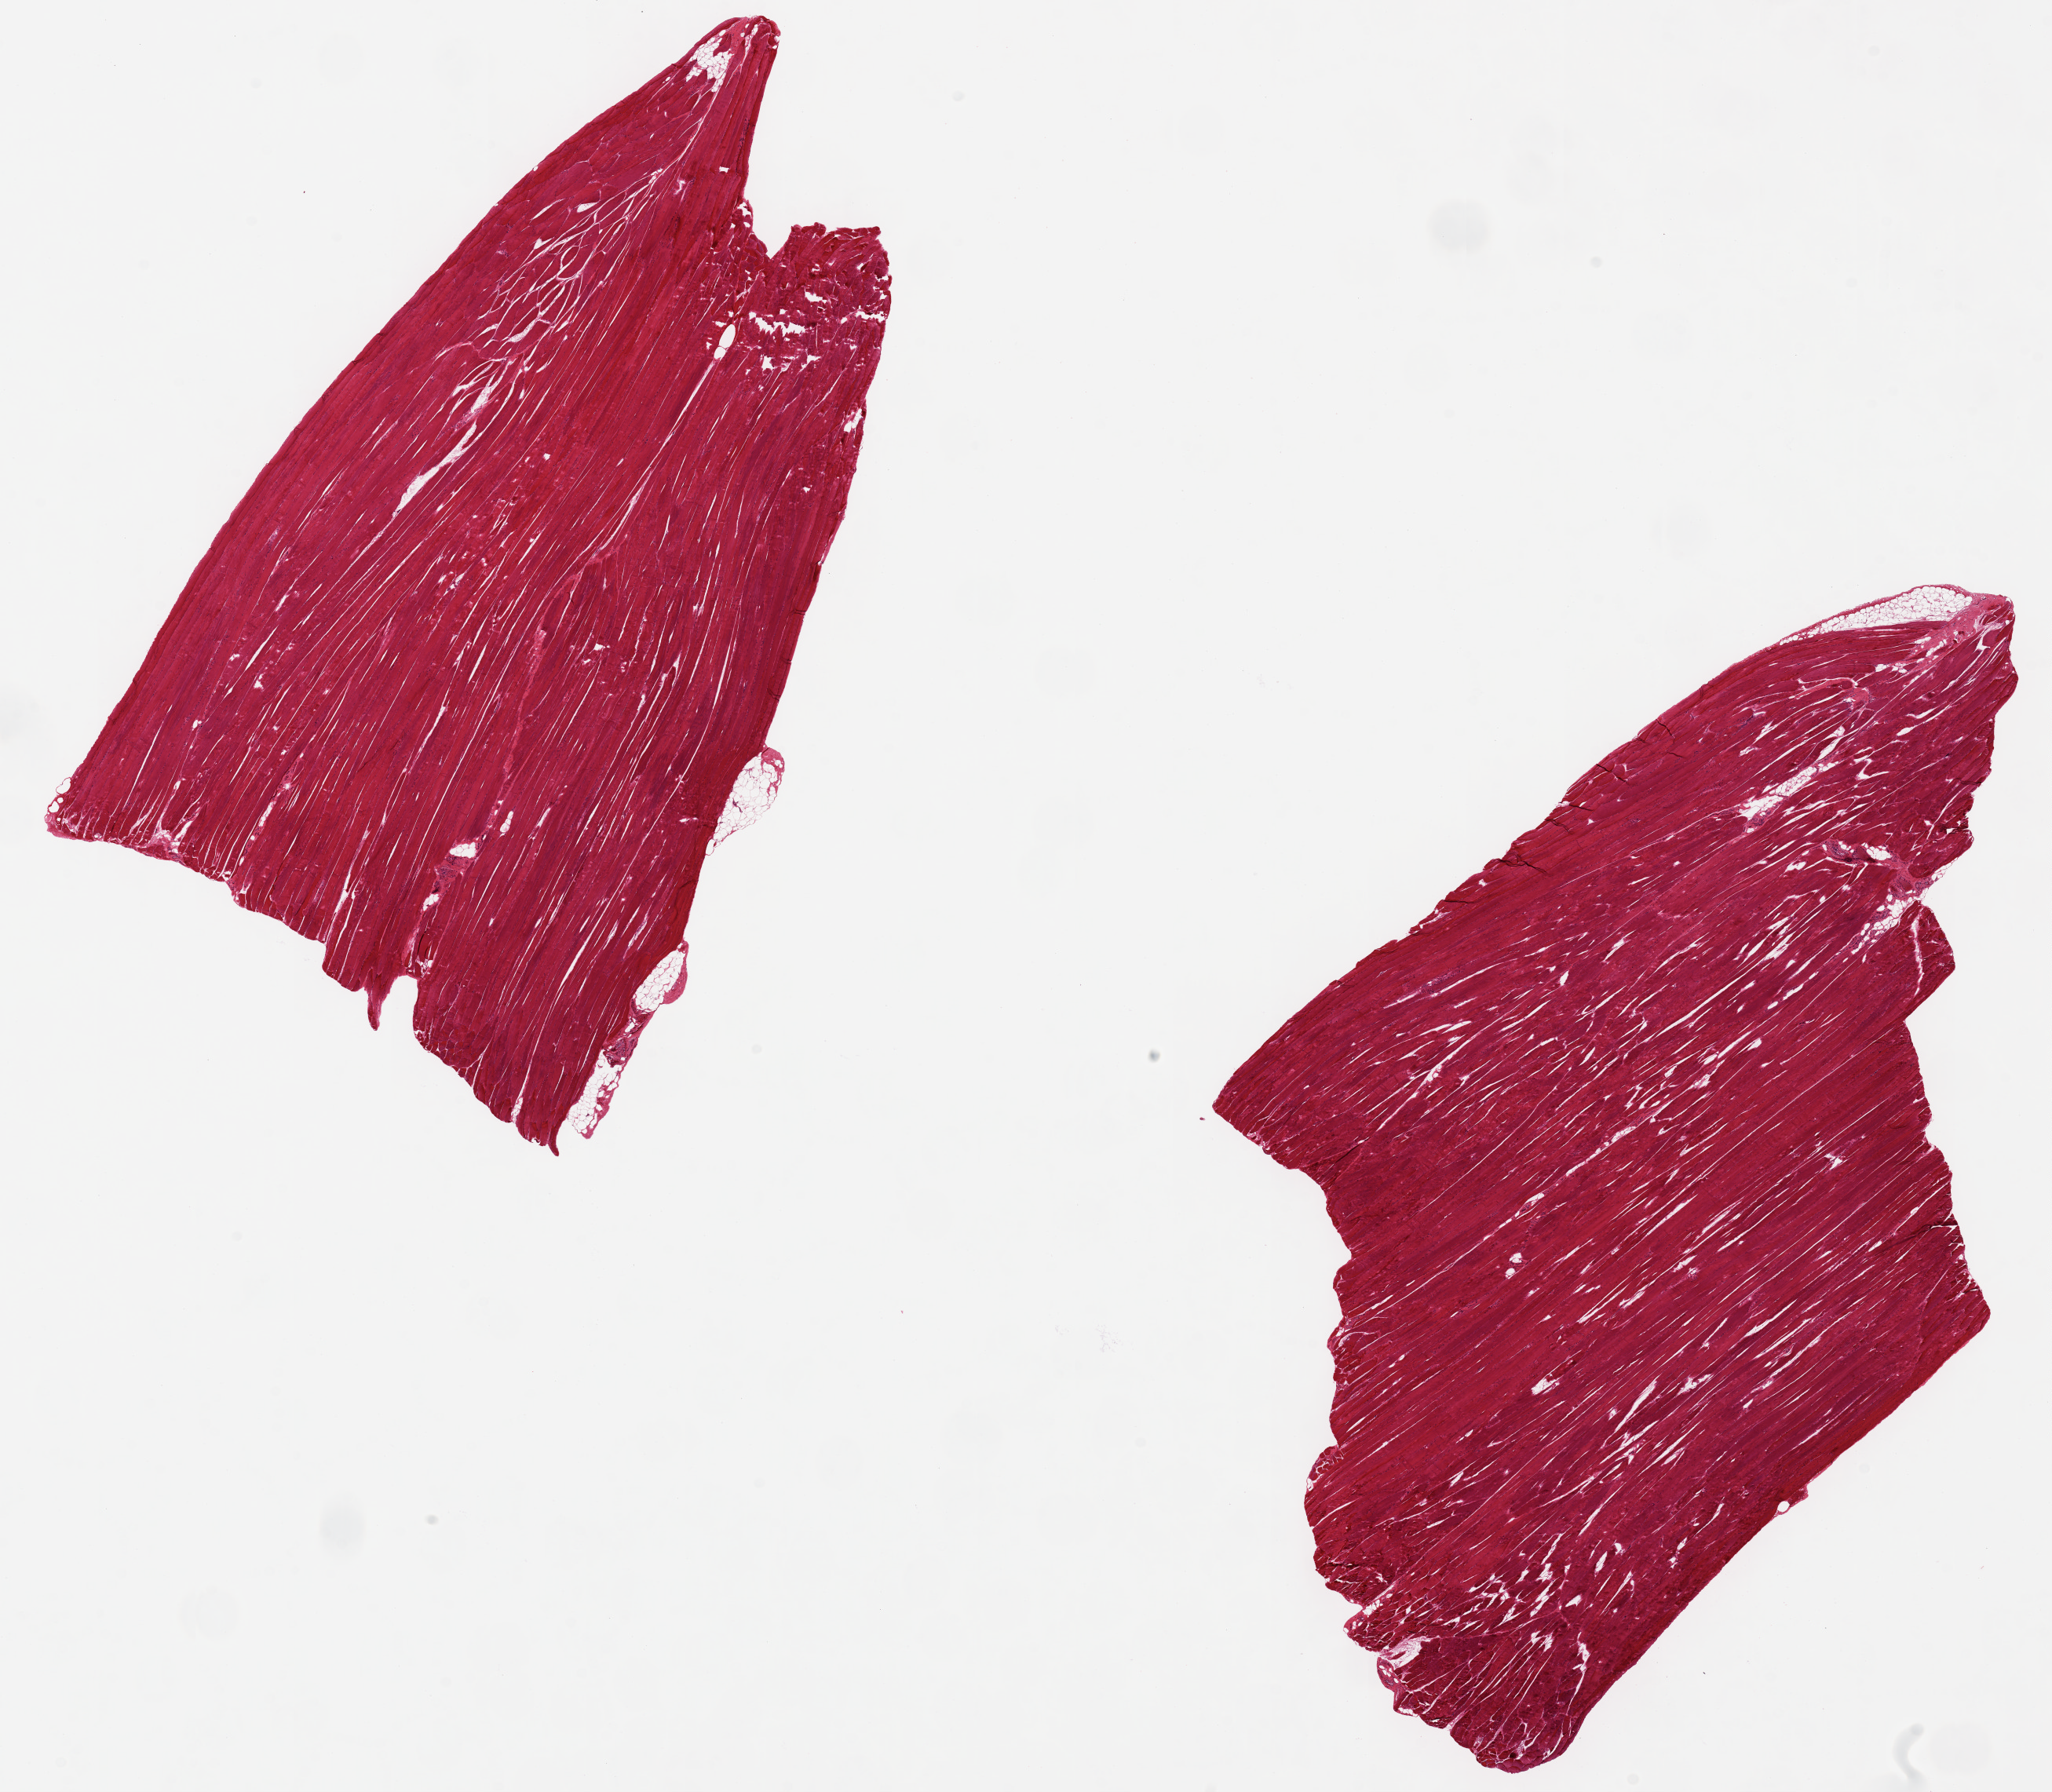
Digitized haematoxylin and eosin-stained section — a low-resolution overview of the entire scanned area, about 20.7 x 18.1 mm (acquisition: 20x scan), PAXgene-fixed, paraffin-embedded tissue, section of skeletal muscle (target tissue), tissue donor sample. Male donor.
Pathologist's review note for this sample: 2 pieces, 11x6 & 9.5x8mm; striations retained despite fragmentation.